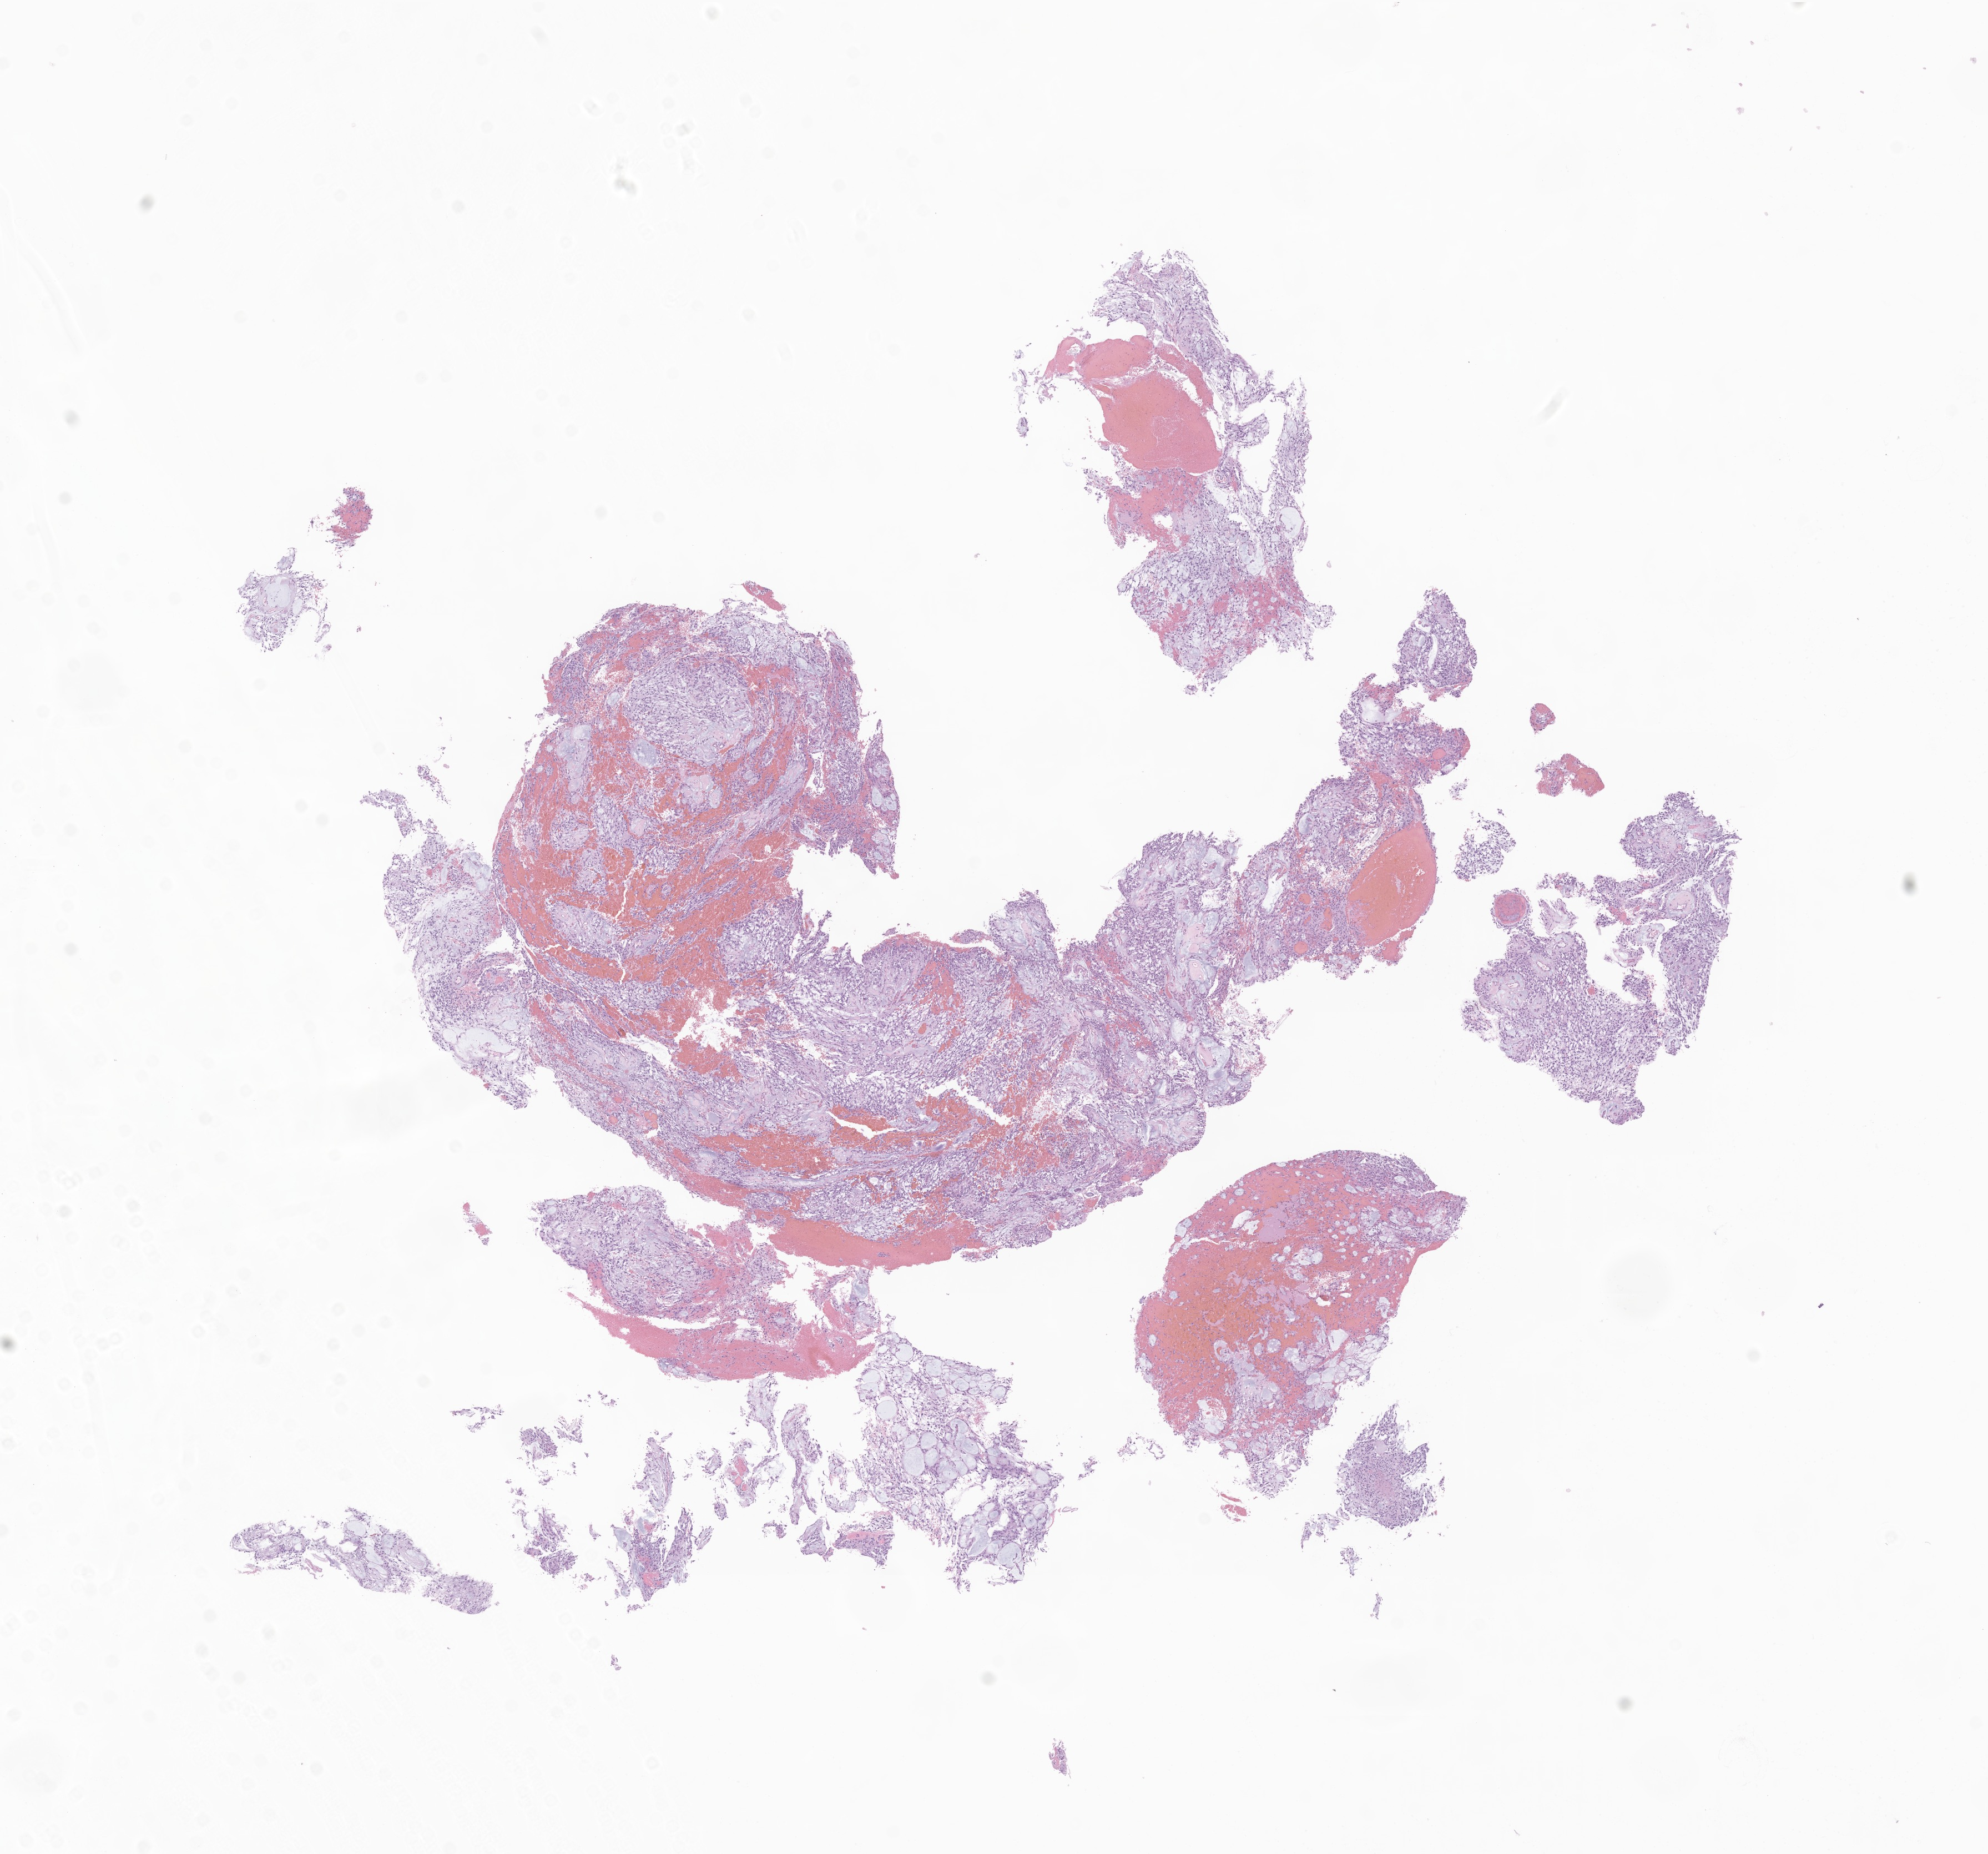
Hematoxylin and eosin (H&E) whole-slide image of tumor tissue from the spinal cord, shown as a low-resolution overview of the whole scanned area (about 15.1 x 14.1 mm), FFPE section. Patient: male, age 118 months.
Diagnosis (ICD-O-3 morphology term): Myxopapillary ependymoma.